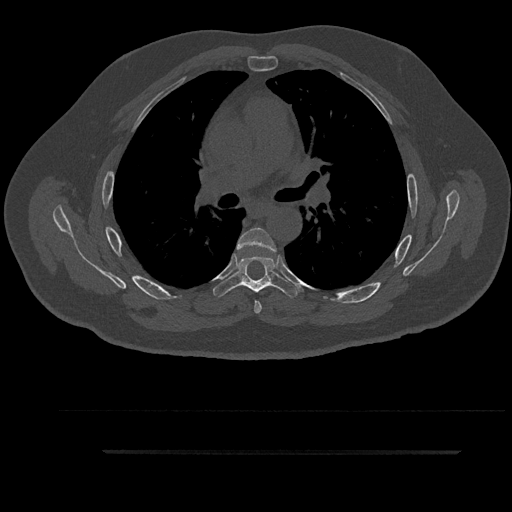
CT including the spine, one axial slice. Slice 596 of 797 in the series (ordered by position). Reconstruction kernel Br40s/3. Bone window (W 1800 / L 400 HU). 0.5 mm slice thickness. 512 × 512 image matrix. Patient: male, 63 years. From the clinical record (not read from this slice): primary cancer: renal.
Outlined on this slice (semi-automatic segmentation, software-assisted and operator-edited):
- T5 vertebra: box from (x=237, y=227) to (x=276, y=314) px
- T6 vertebra: (x=213, y=256)–(x=300, y=297)